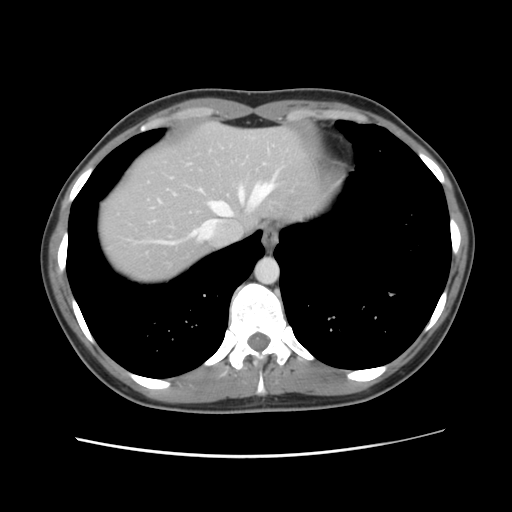
Contrast-enhanced abdominal CT, one axial slice; slice 106 of 134 in the series (ordered by position); soft-tissue window (W 400 / L 40 HU); 512 × 512 image matrix. Female patient, age 33 years. Case-level facts recorded for this patient, not image findings: diagnosis: colorectal cancer liver metastases, imaged before liver resection; multiple liver metastases: yes; largest metastasis: 4.5 cm; disease in both lobes: yes.
Structures marked on this image (outlined manually by an expert reader):
- hepatic veins: bounding box <160,177,276,244> (left, top, right, bottom; pixels)
- liver: <98,122,324,284>
- planned liver remnant (the part of the liver to remain after resection): <98,122,323,284>